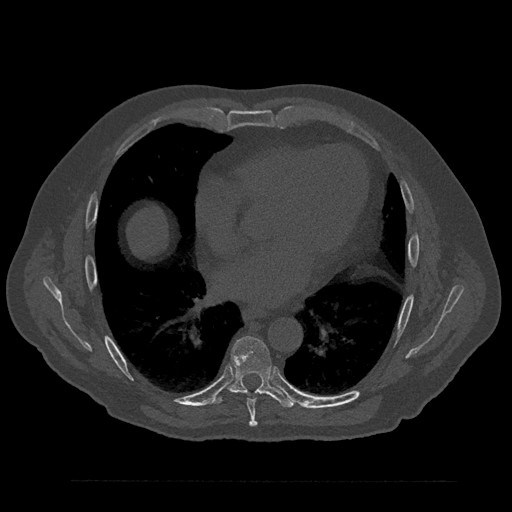
CT including the spine, one axial slice; slice 475 of 797 in the series (ordered by position); 120 kVp; bone window (W 1800 / L 400 HU); 0.5 mm slice thickness; 512 × 512 image matrix, field of view 430 × 430 mm. Male patient, age 61 years. From the clinical record (not read from this slice): primary cancer: prostate.
Outlined on this slice (semi-automatic segmentation, software-assisted and operator-edited):
- T7 vertebra: bounding box <242,390,258,427> (left, top, right, bottom; pixels)
- T8 vertebra: <214,336,295,408>